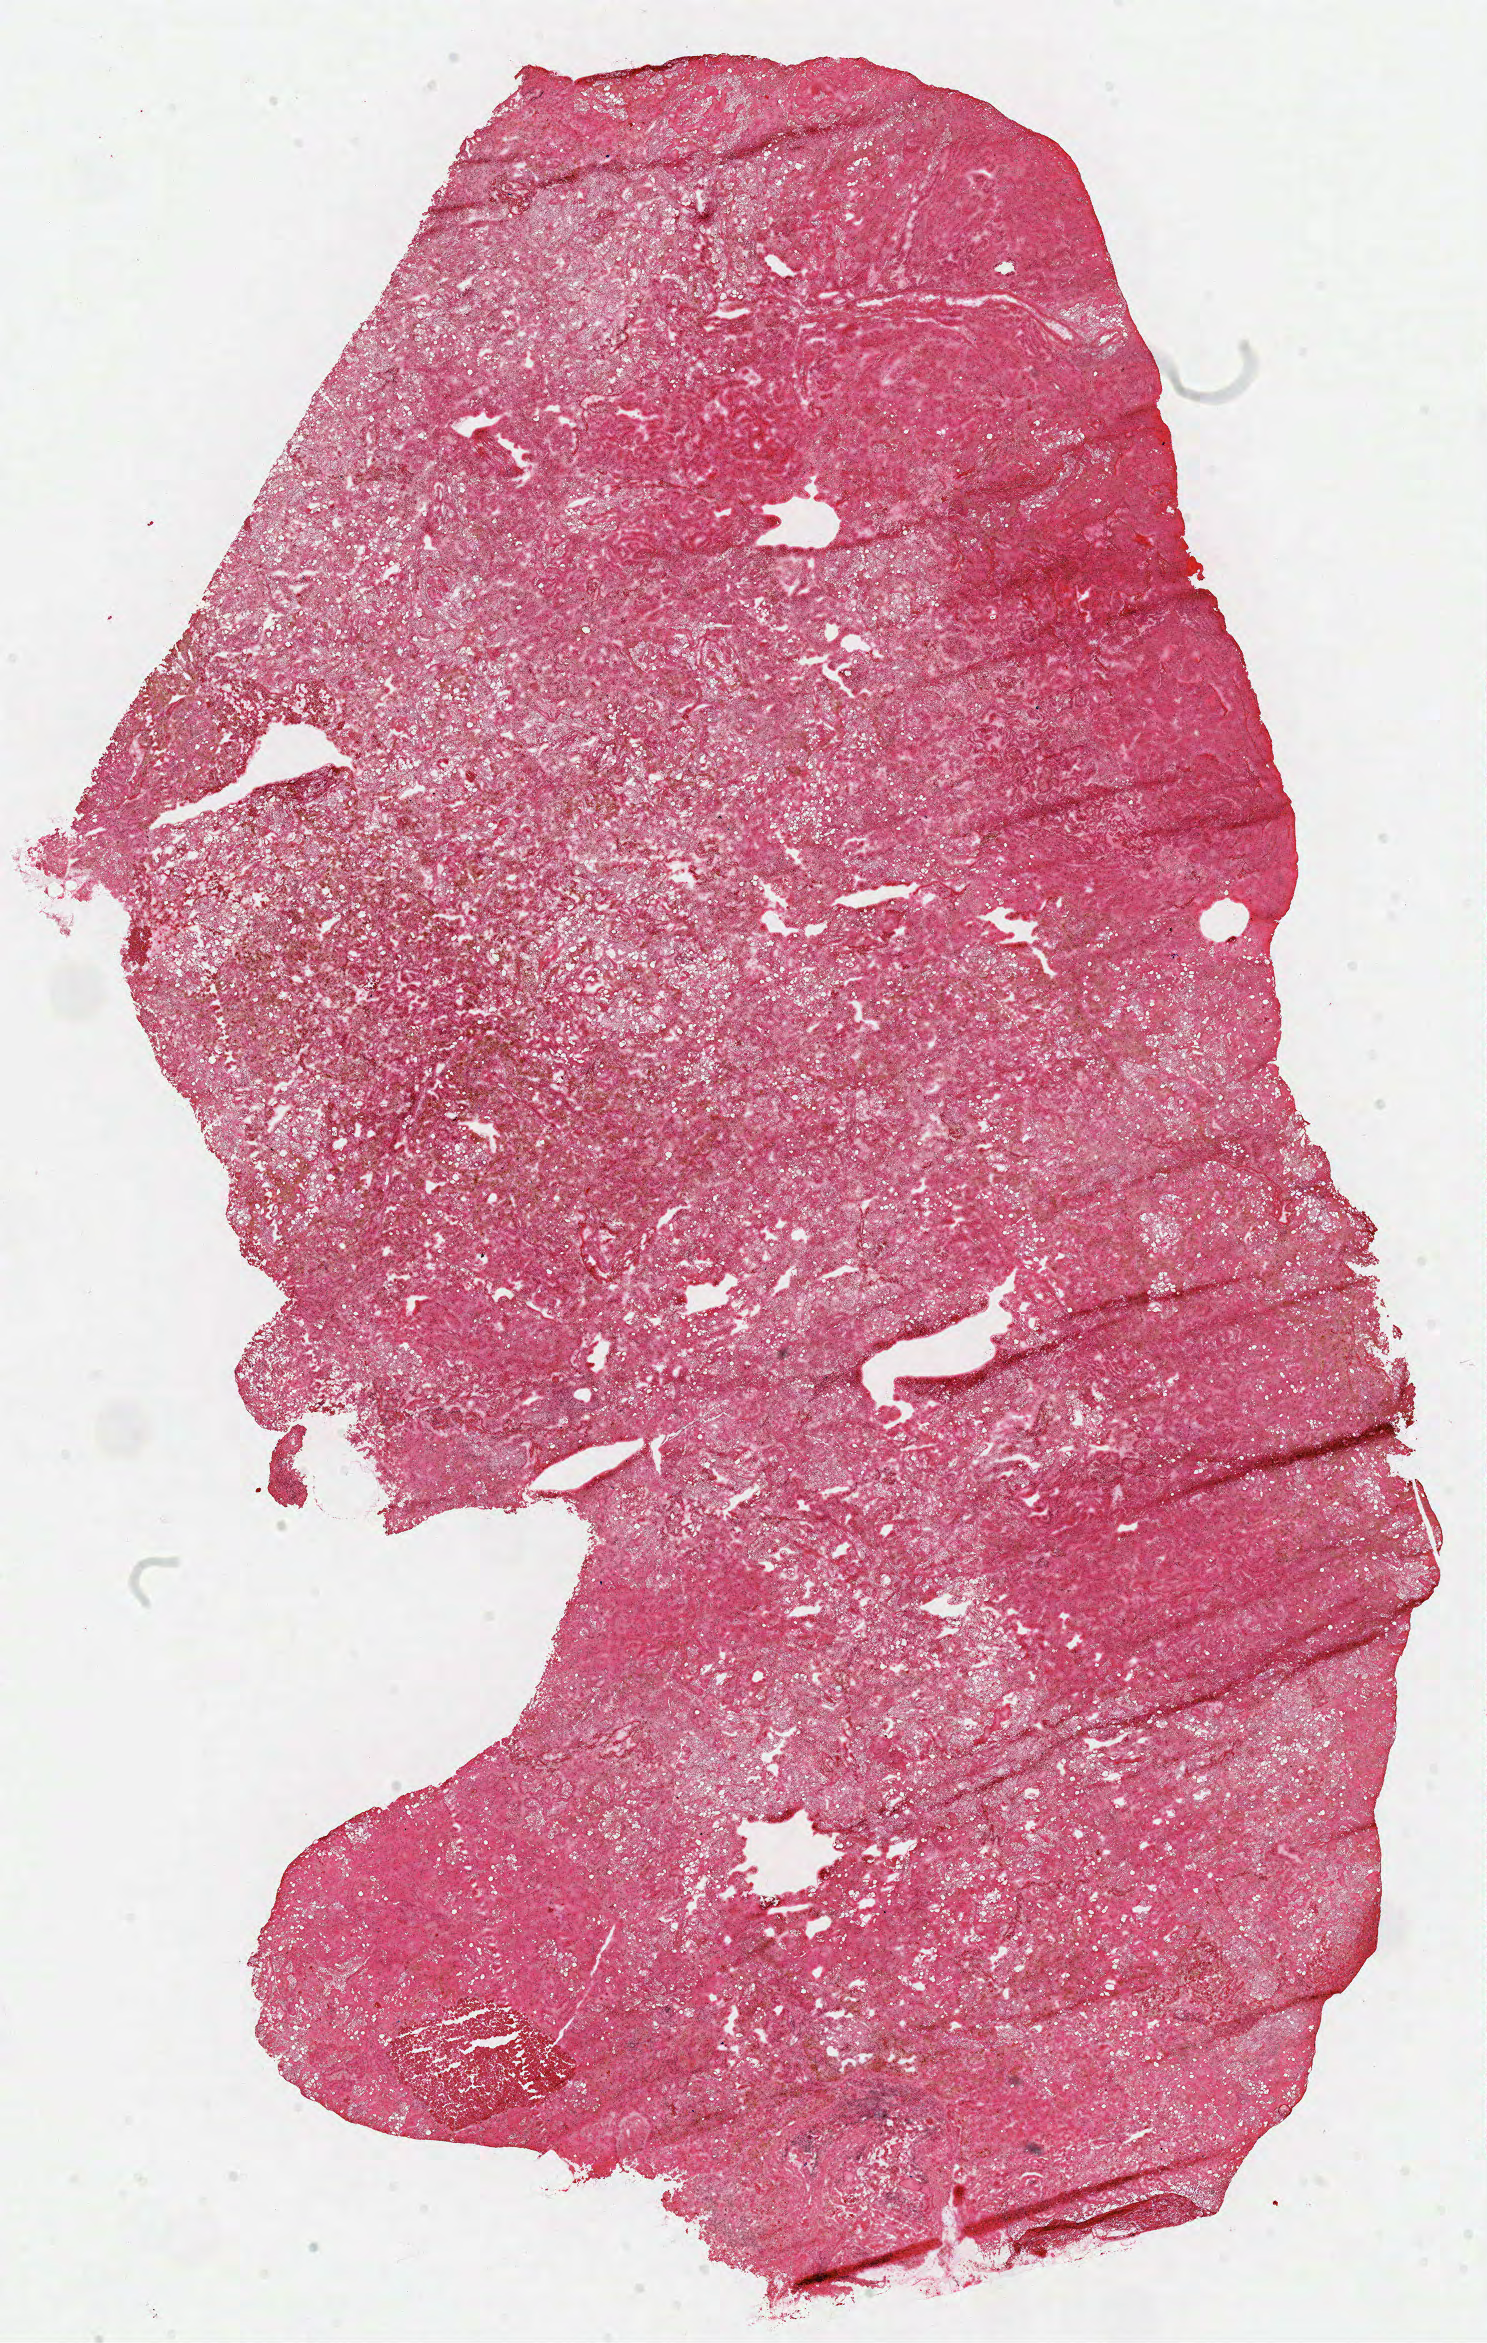
Digitized H&E tissue section (whole slide) — shown as a low-resolution overview of the whole scanned area (about 11.7 x 18.5 mm, slide scanned at 40x). Frozen section from the top of the tissue portion. Sample: primary tumour, kidney. Male patient; age at initial diagnosis 69 years.
Pathologic diagnosis: Papillary adenocarcinoma, NOS.